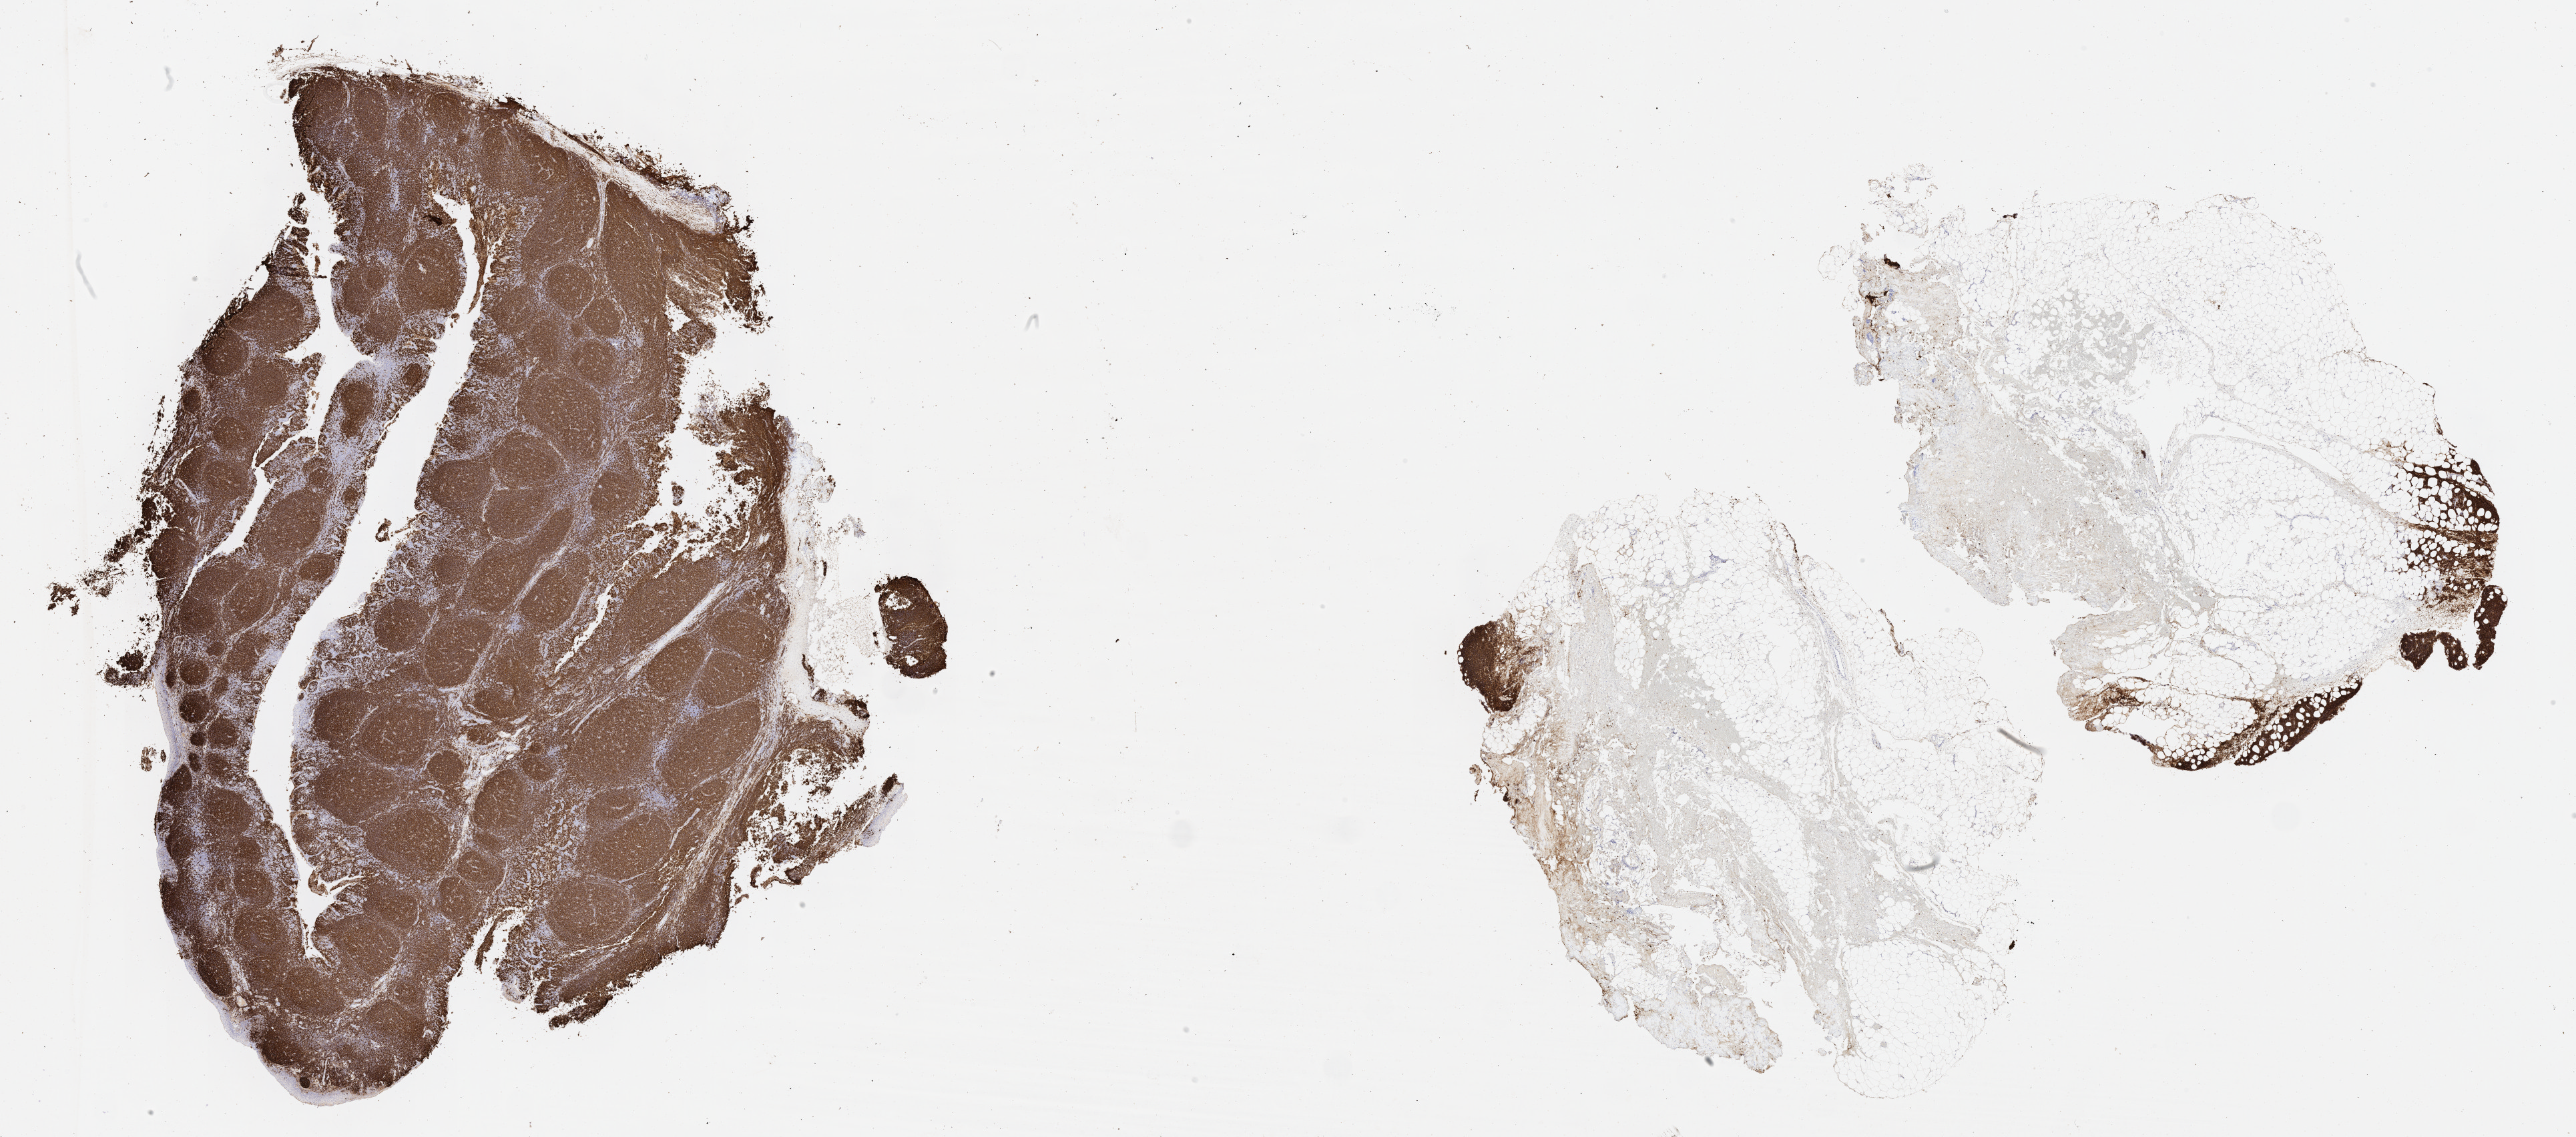
Whole-slide image, immunohistochemical stain for CD20, low-resolution overview of the scanned area, about 31.2 x 13.8 mm. Tumor tissue. Anatomic site: upper limb lymph node. Male patient, age 76 years.
Diagnosis: Burkitt lymphoma, NOS.